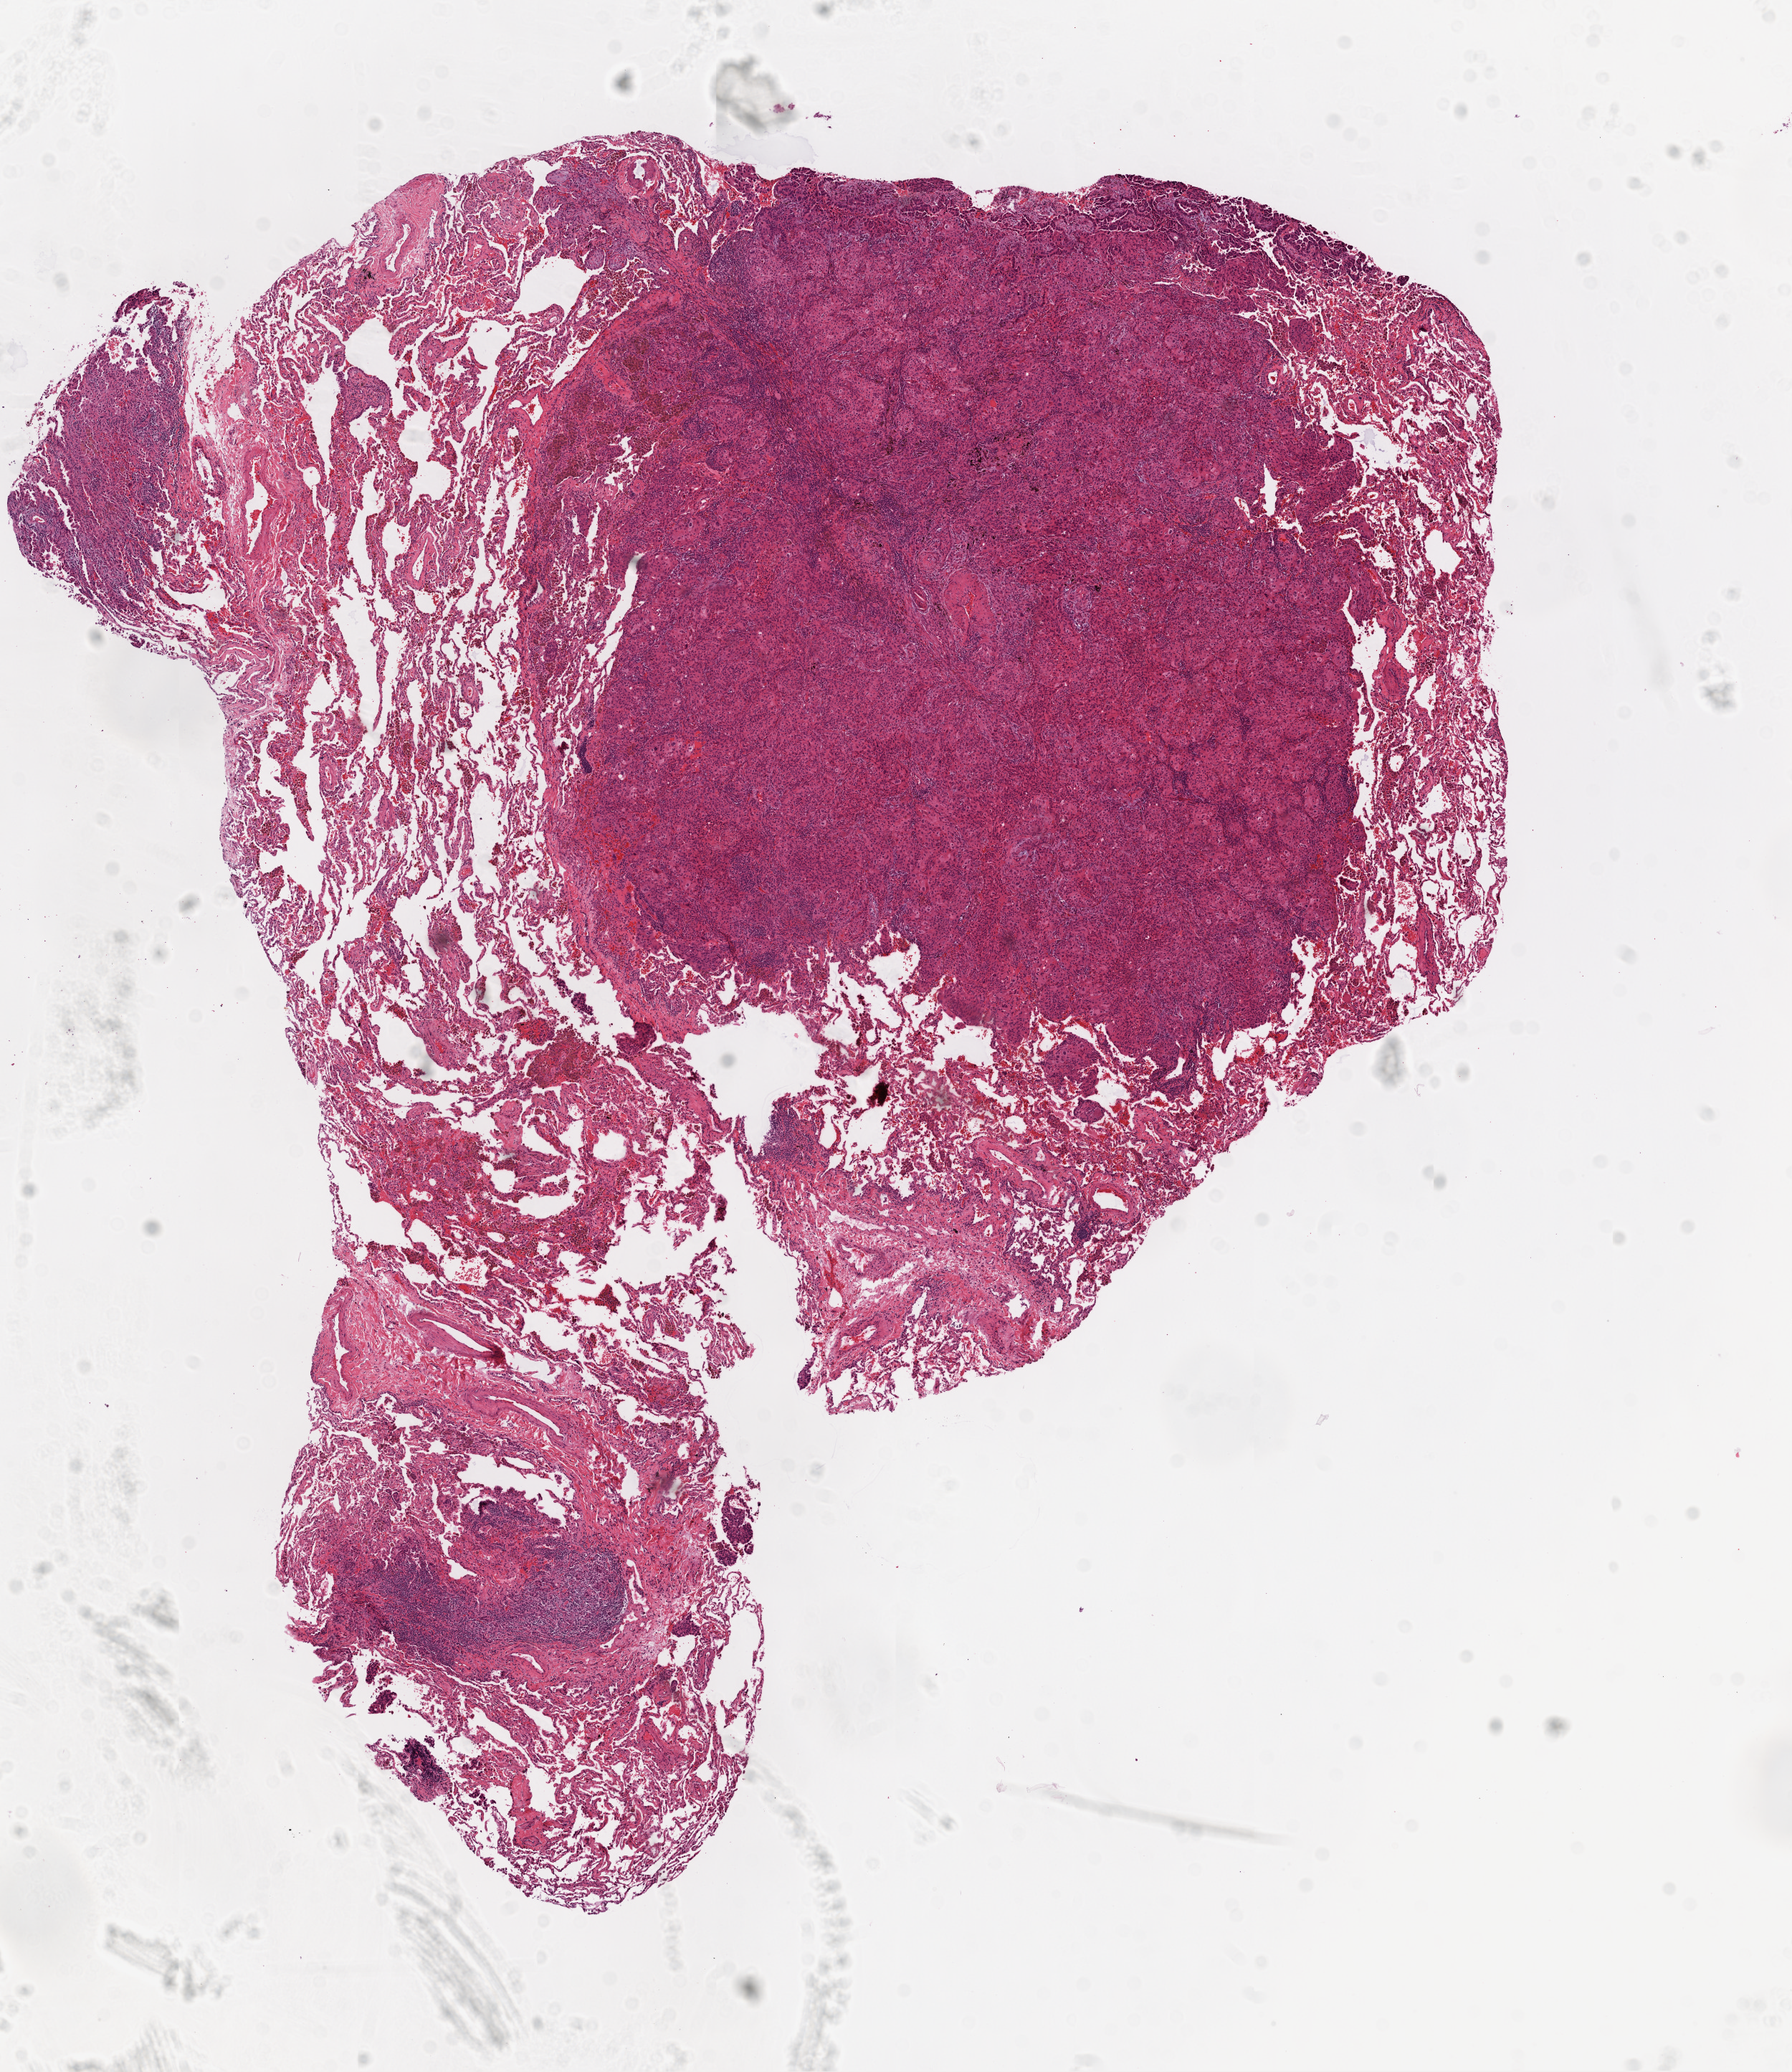
H&E whole-slide image — whole scanned area (about 10.0 x 11.6 mm) shown as a low-resolution overview; frozen section; lung, primary tumour sample. Male patient; age at initial diagnosis 59 years. Slide review estimates, as recorded: tumour cells 50%, tumour nuclei 50%, normal cells 50%, stromal cells 0%, necrosis 0%. Inflammatory infiltration, as recorded: lymphocyte infiltration 5%.
- pathologic diagnosis: Adenocarcinoma, NOS (upper lobe, lung)
- AJCC pathologic stage: IB (6th edition)
- laterality: right